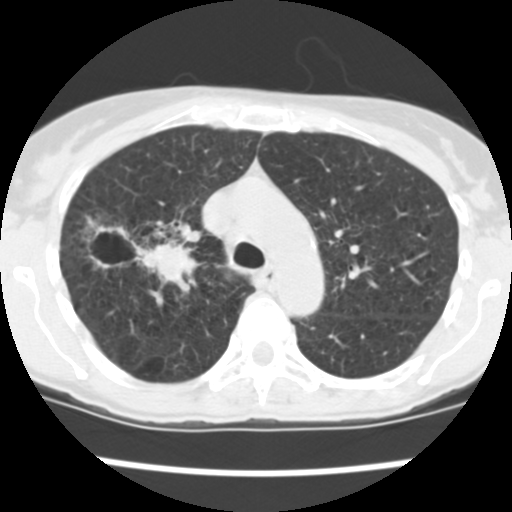
Low-dose screening chest CT, one axial slice; slice 174 of 252 in the series (ordered by position); reconstruction kernel STANDARD; 120 kVp; lung window (W 1500 / L -600 HU); 512 × 512 image matrix, field of view 276 × 276 mm.
Outlined on this slice (manually delineated by an expert):
- lesion 2 (tumor, lower lobe of right lung): bounding box [x1, y1, x2, y2] px = [91, 223, 200, 291]